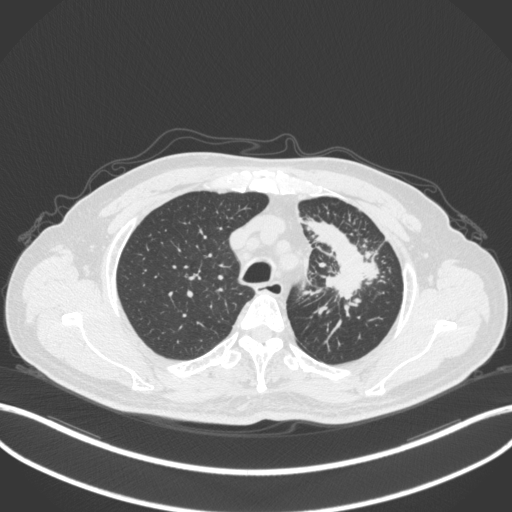
Chest CT, one axial slice. Position 279 of 386 along the scan axis. Reconstruction kernel B31f. 120 kVp. Lung window (W 1500 / L -600 HU). 512 × 512 image matrix, field of view 400 × 400 mm. Patient: male, 69 years. From the clinical record (not read from this slice): clinical TNM (as recorded): T2a N2 M0.
Outlined on this slice (rectangle marked by the reading radiologist):
- lung tumour (recorded histology: adenocarcinoma): bounding box [x1, y1, x2, y2] px = [305, 214, 394, 304]